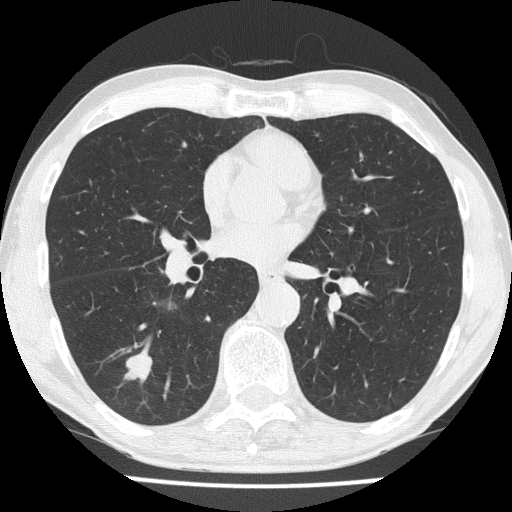
Low-dose screening chest CT, axial slice; third screening round (two years after baseline); lung window (W 1500 / L -600 HU). Male, age 59 years at enrolment. Former smoker at enrolment.
• Expert-annotated lung lesion, bounding box [x1, y1, x2, y2] px = [112, 346, 159, 392].
• Screening reader's record for this exam (one nodule recorded; not confirmed to be the boxed lesion): non-calcified nodule or mass ≥4 mm, right lower lobe, 20 × 16 mm, smooth margins, soft tissue attenuation, pre-existing on the prior screen: no.
• Official screen result: positive, other.
• Participant outcome: lung cancer diagnosed 25 days after this screen — small cell carcinoma, NOS, right lower lobe, stage IIA (AJCC 6th edition), 20 mm at pathology.